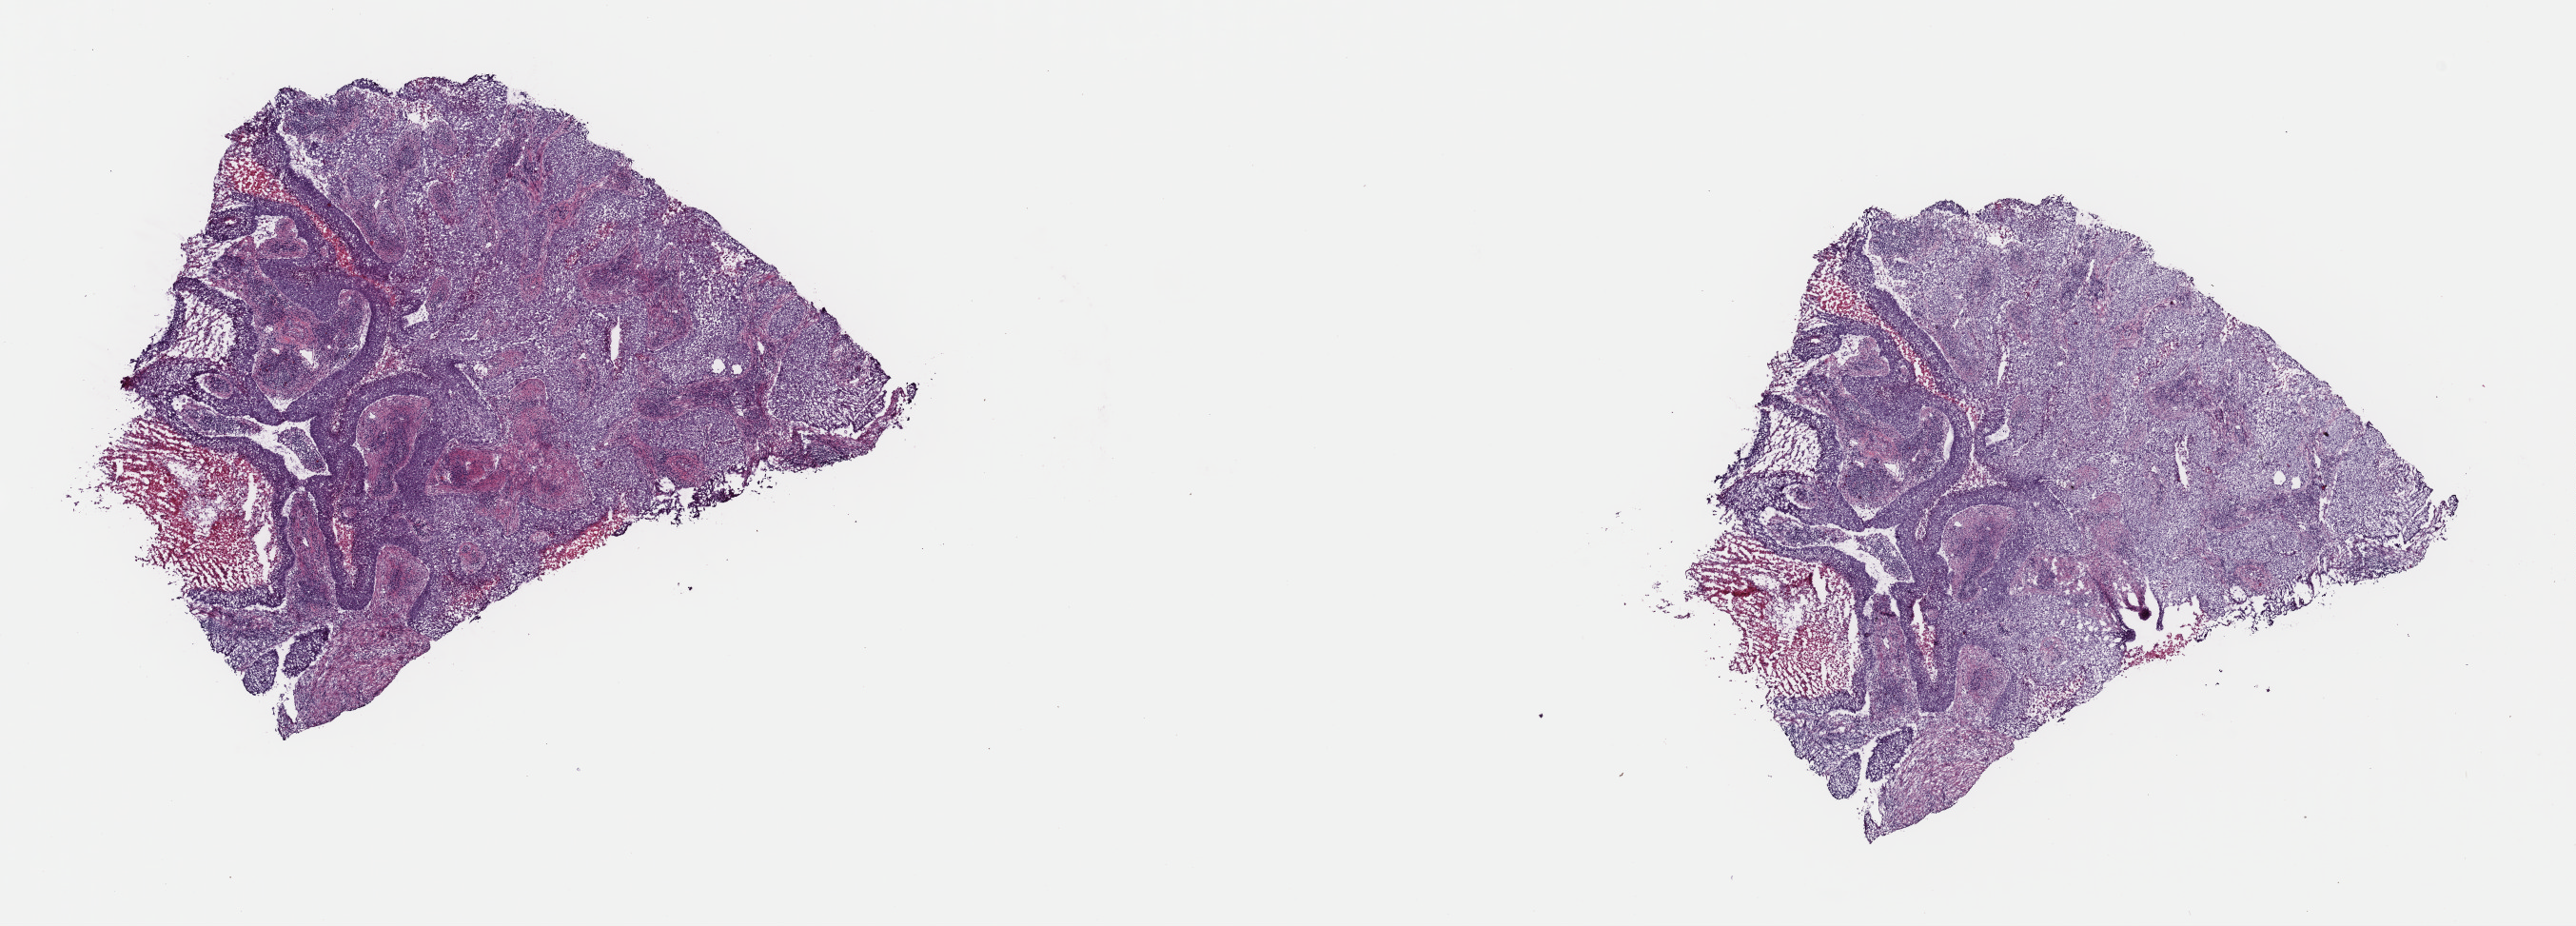
Whole-slide histology image, Hematoxylin and eosin (H&E) stained — shown as a low-resolution overview of the whole scanned area (about 21.4 x 7.7 mm, slide scanned at 40x); frozen section from the top of the tissue portion; lung, primary tumour sample. Patient: male, age at initial diagnosis 59 years. Composition of this section per pathologist review: tumour cells 50%, tumour nuclei 85%, normal cells 0%, stromal cells 30%, necrosis 20%. Infiltration values recorded for this section: lymphocyte infiltration 5%, monocyte infiltration 5%, neutrophil infiltration 2%.
Pathologic diagnosis: Basaloid squamous cell carcinoma. Laterality: right. TNM: T2 N2 M0. AJCC pathologic stage: IIIA (6th edition).